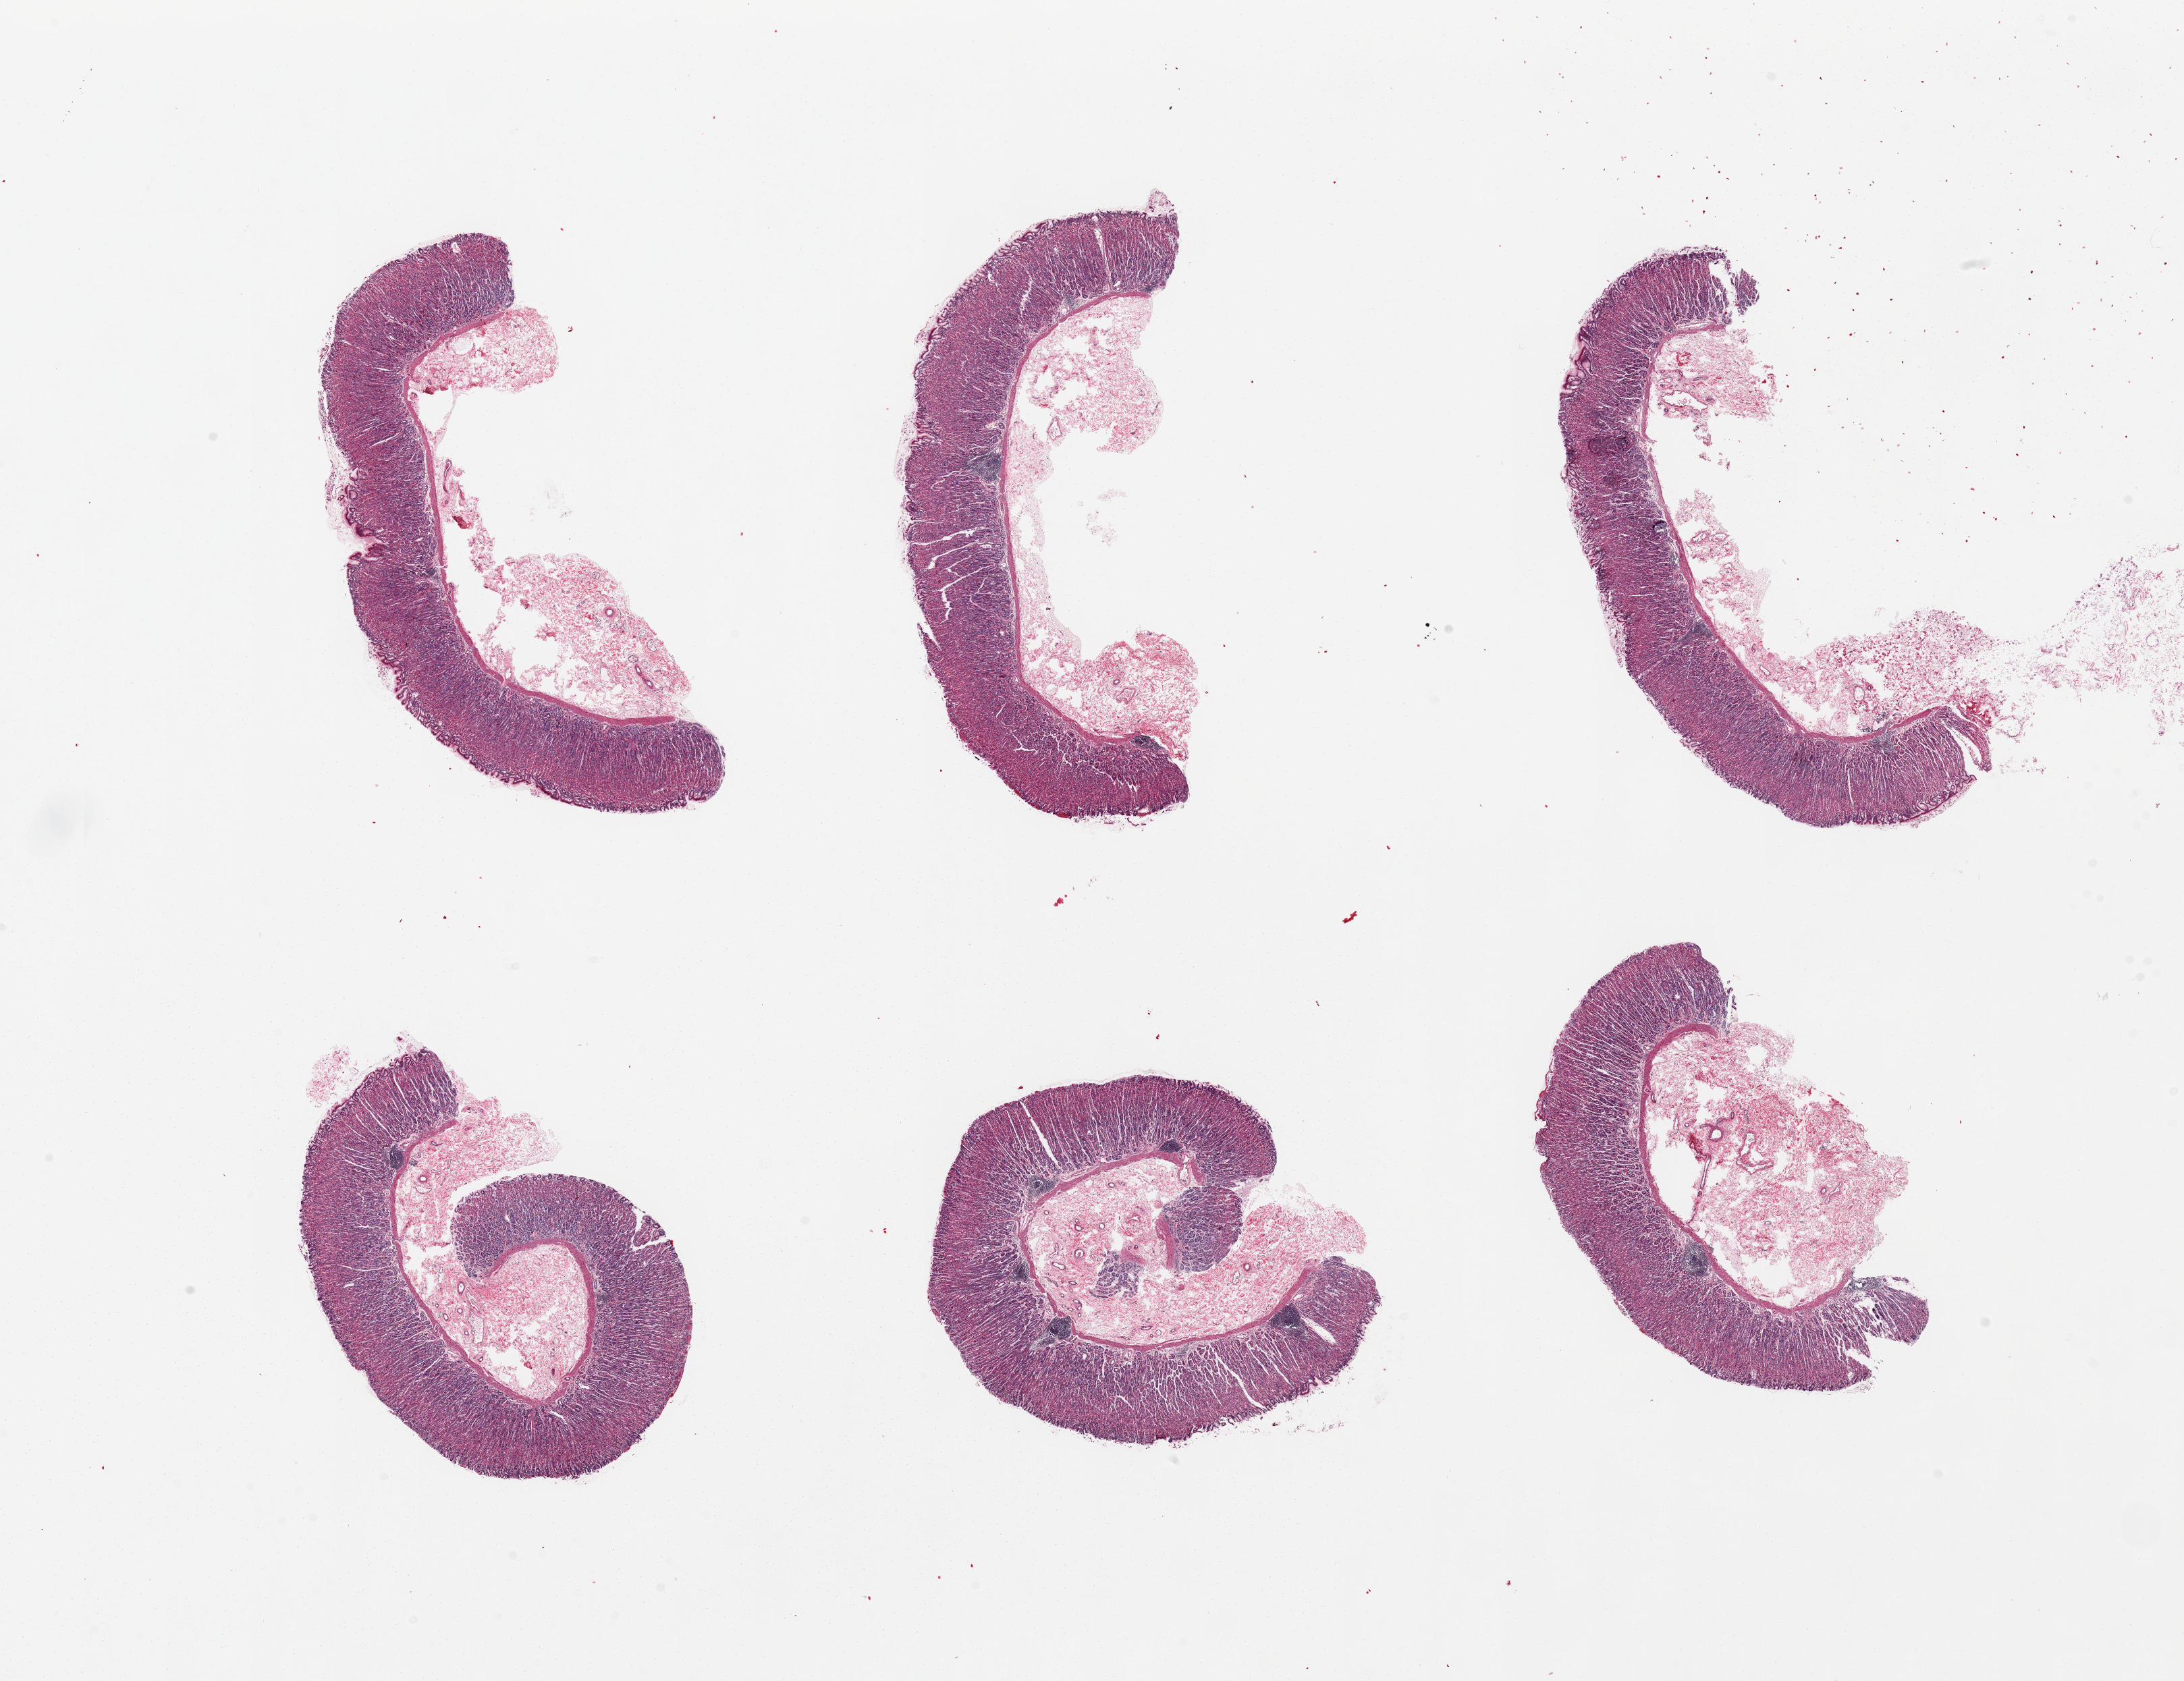
Hematoxylin and eosin (H&E) whole-slide image — shown as a low-resolution overview of the whole scanned area (about 25.6 x 19.7 mm). PAXgene-fixed, paraffin-embedded tissue. Section of stomach (target tissue). Tissue donor sample. Male donor.
Pathologist's review note for this sample: 6 pieces, beautifully preserved, mucosa up to 1mm thick in all, 80-100% thickness.